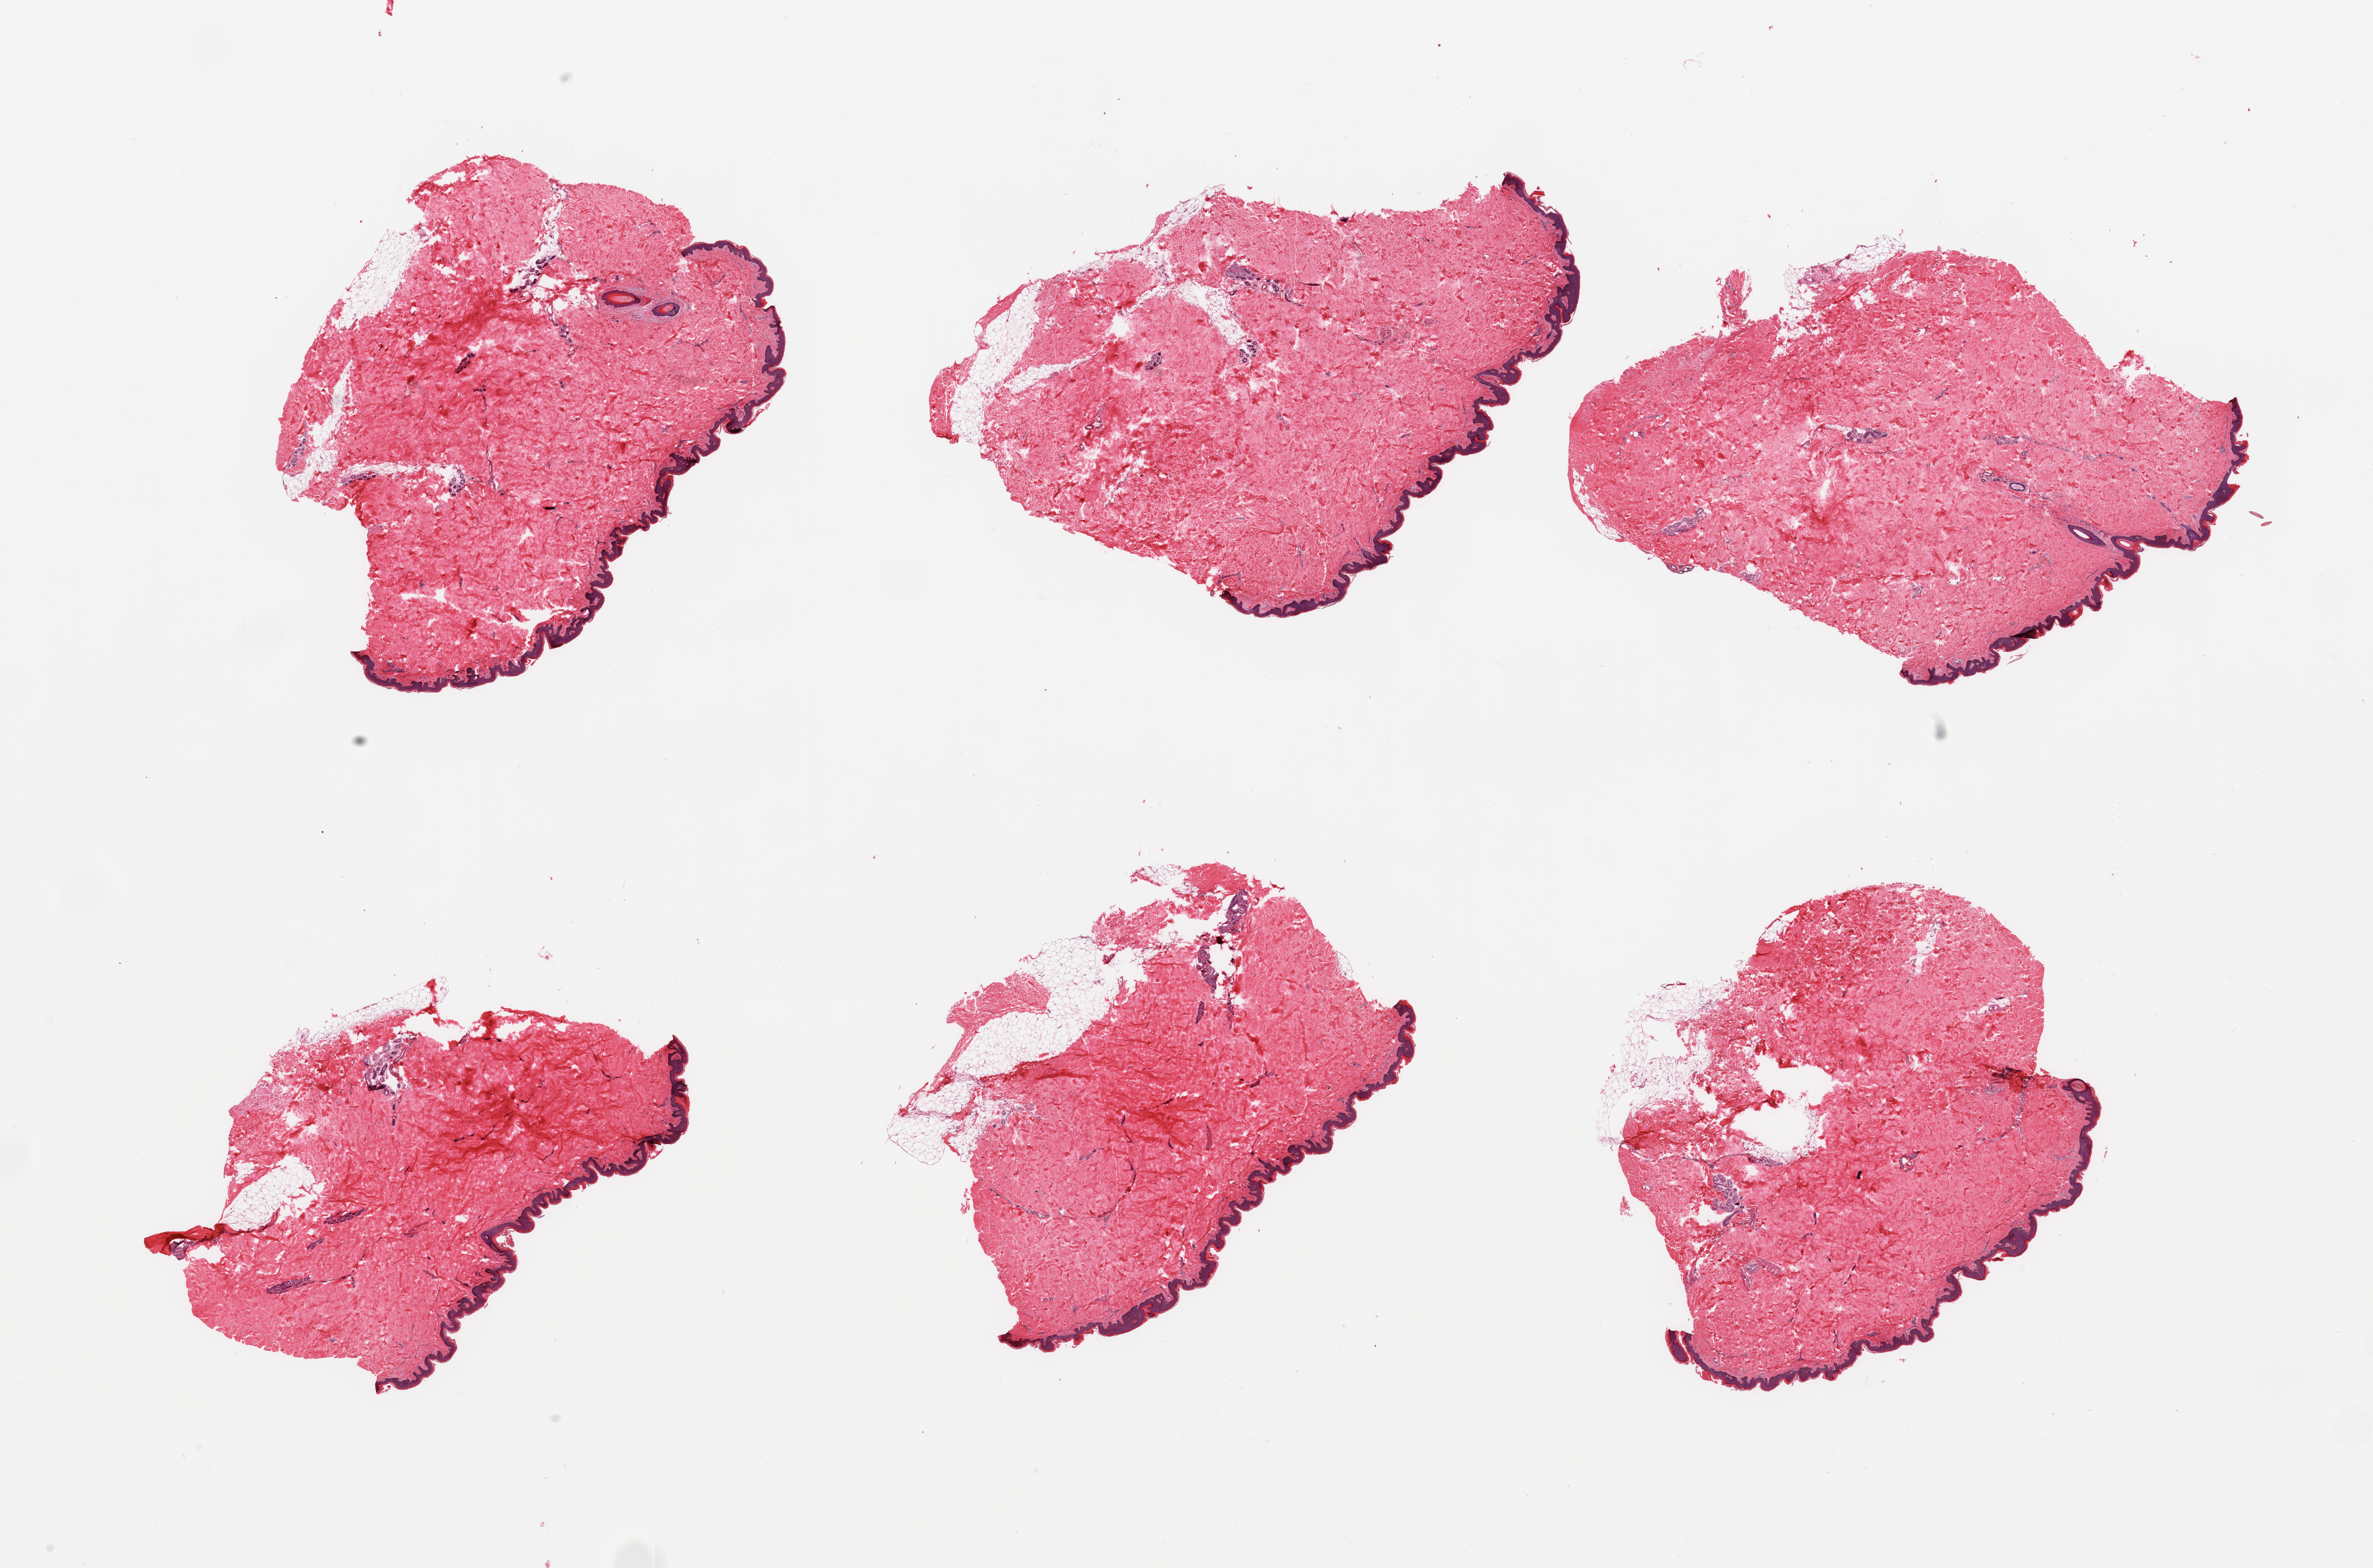
Haematoxylin and eosin whole-slide image, low-resolution overview of the scanned area, about 28.5 x 18.9 mm (from a 20x scan). PAXgene-fixed, paraffin-embedded tissue. Target tissue: skin of suprapubic region. Donor tissue sample. Male donor.
Review note (as recorded): 6 pieces; includes <10% internal/external fat.